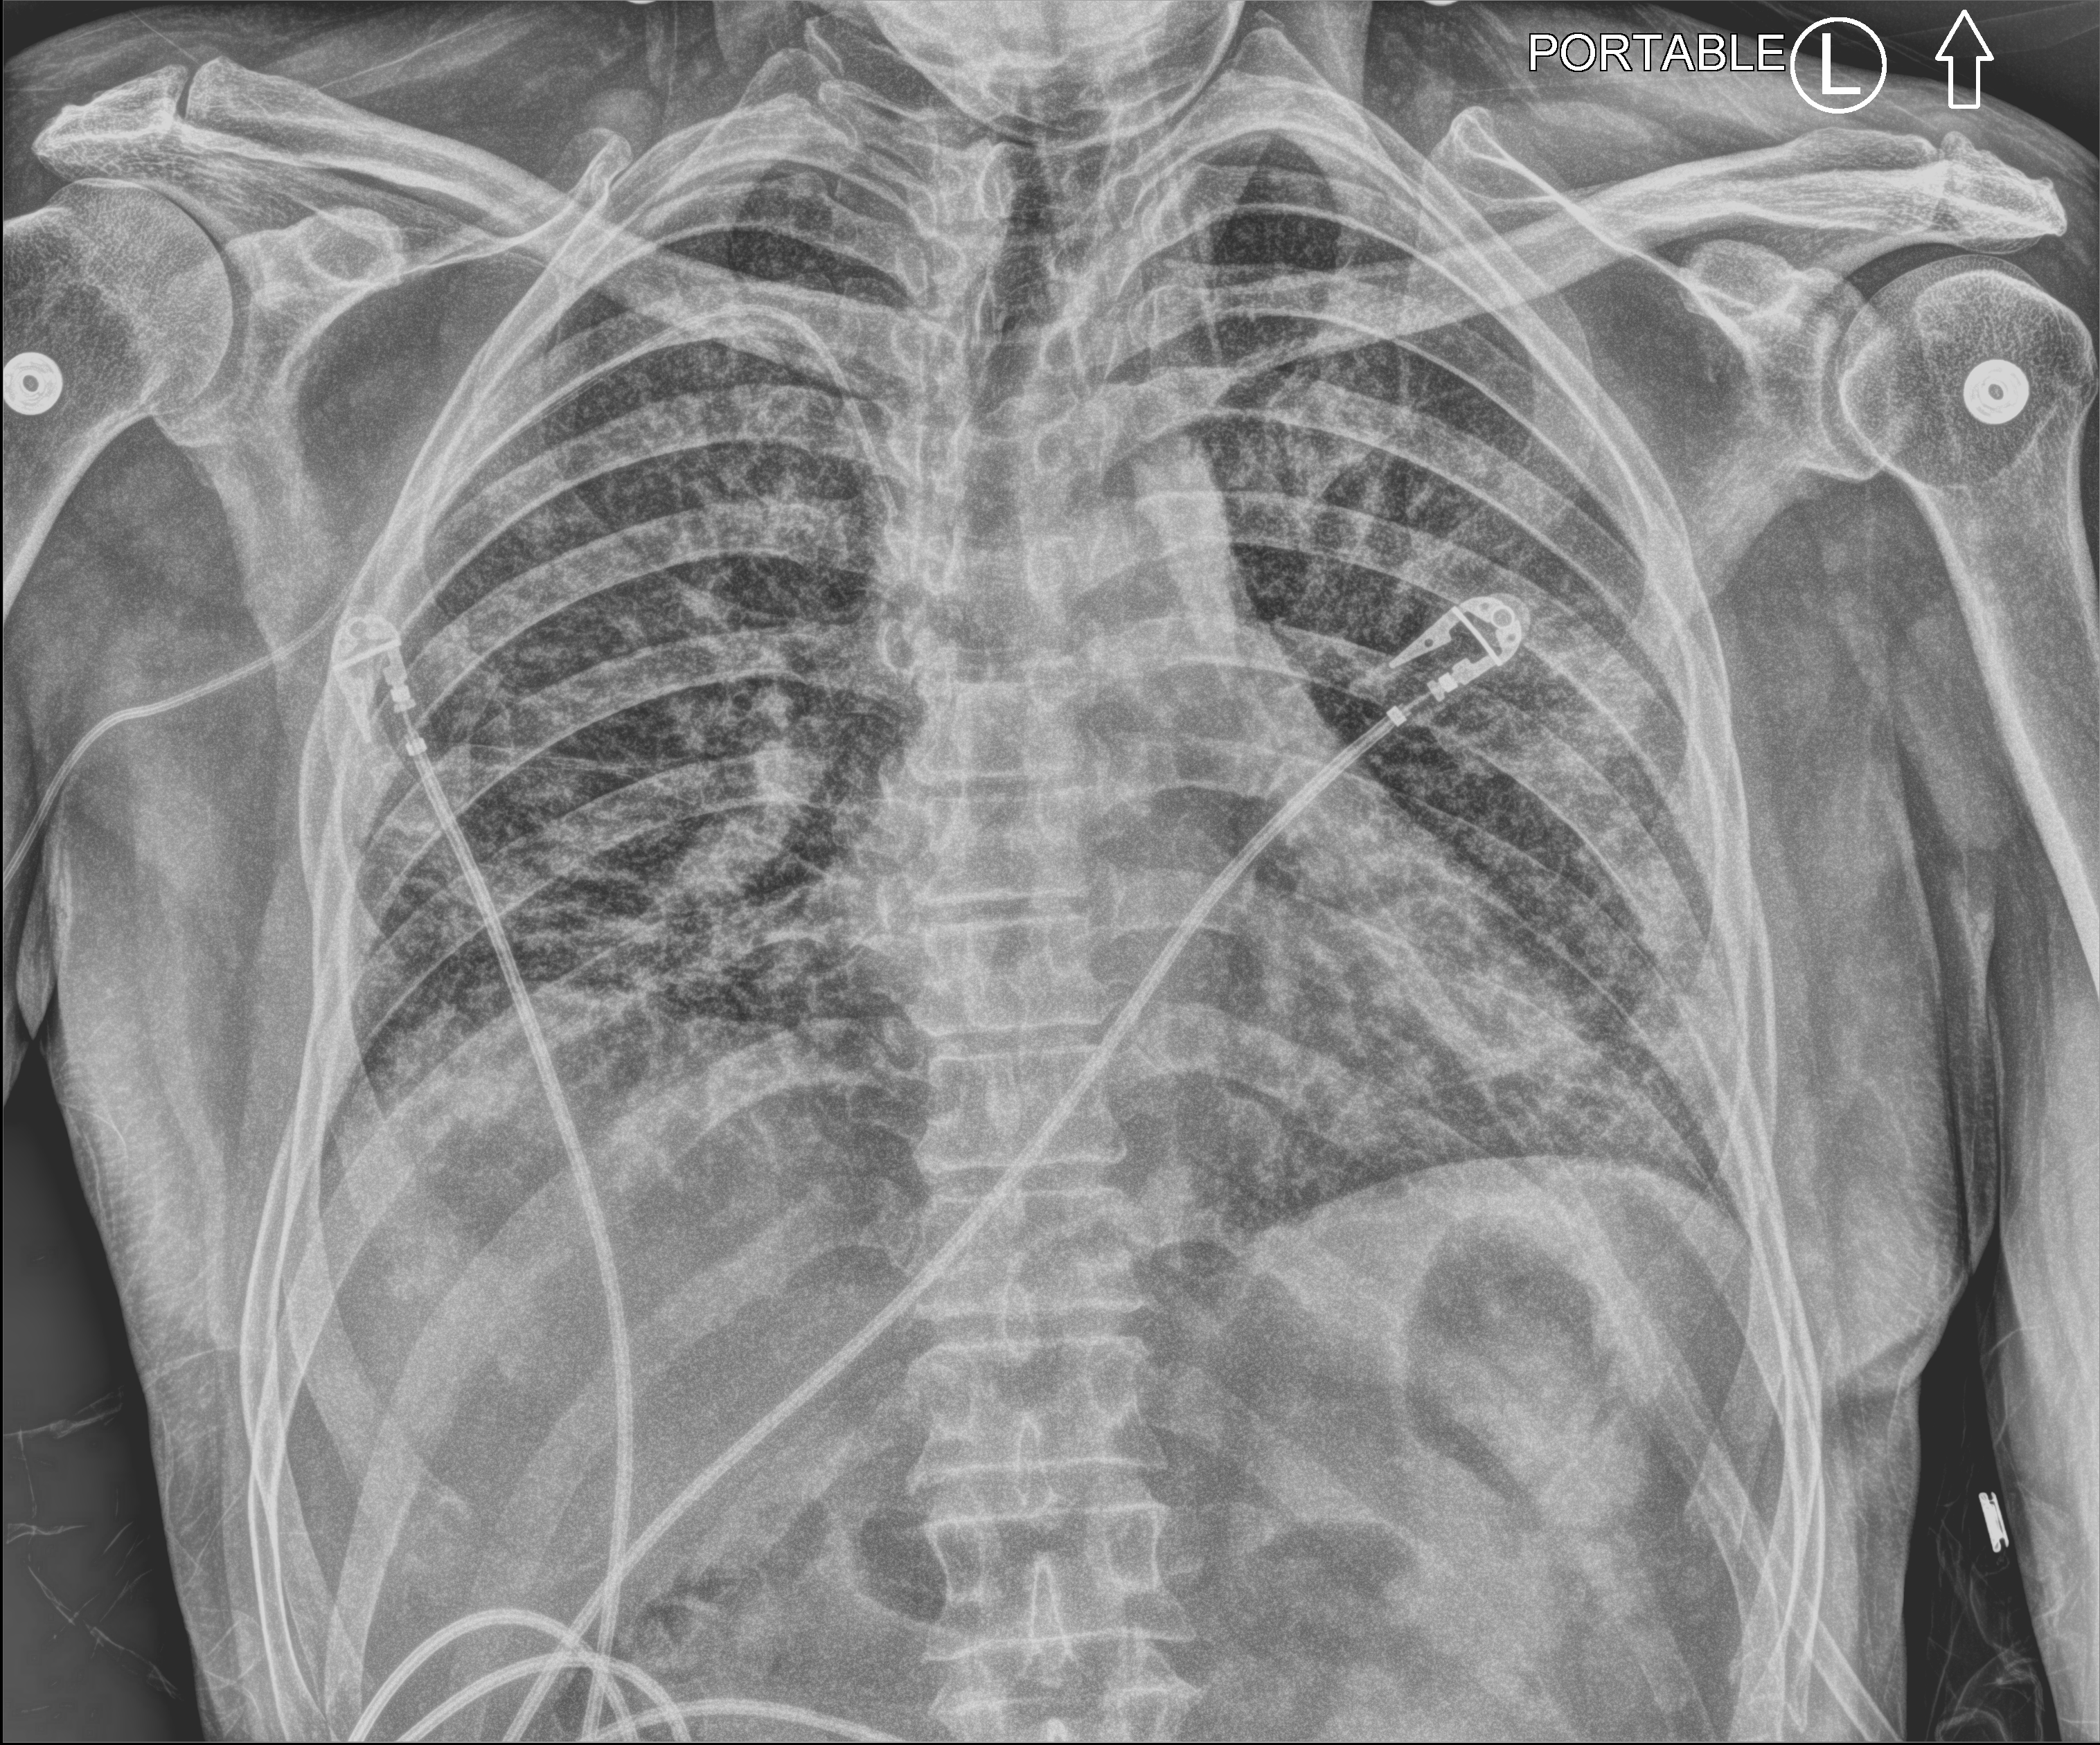
Portable chest radiograph, anteroposterior (AP) projection. Male patient hospitalised with COVID-19, age 18–59 years.
From the hospital-stay record, not from the radiograph (when in the stay this image was taken is not recorded): admitted to intensive care during this hospital stay: yes; other chronic lung disease (admission record): no.